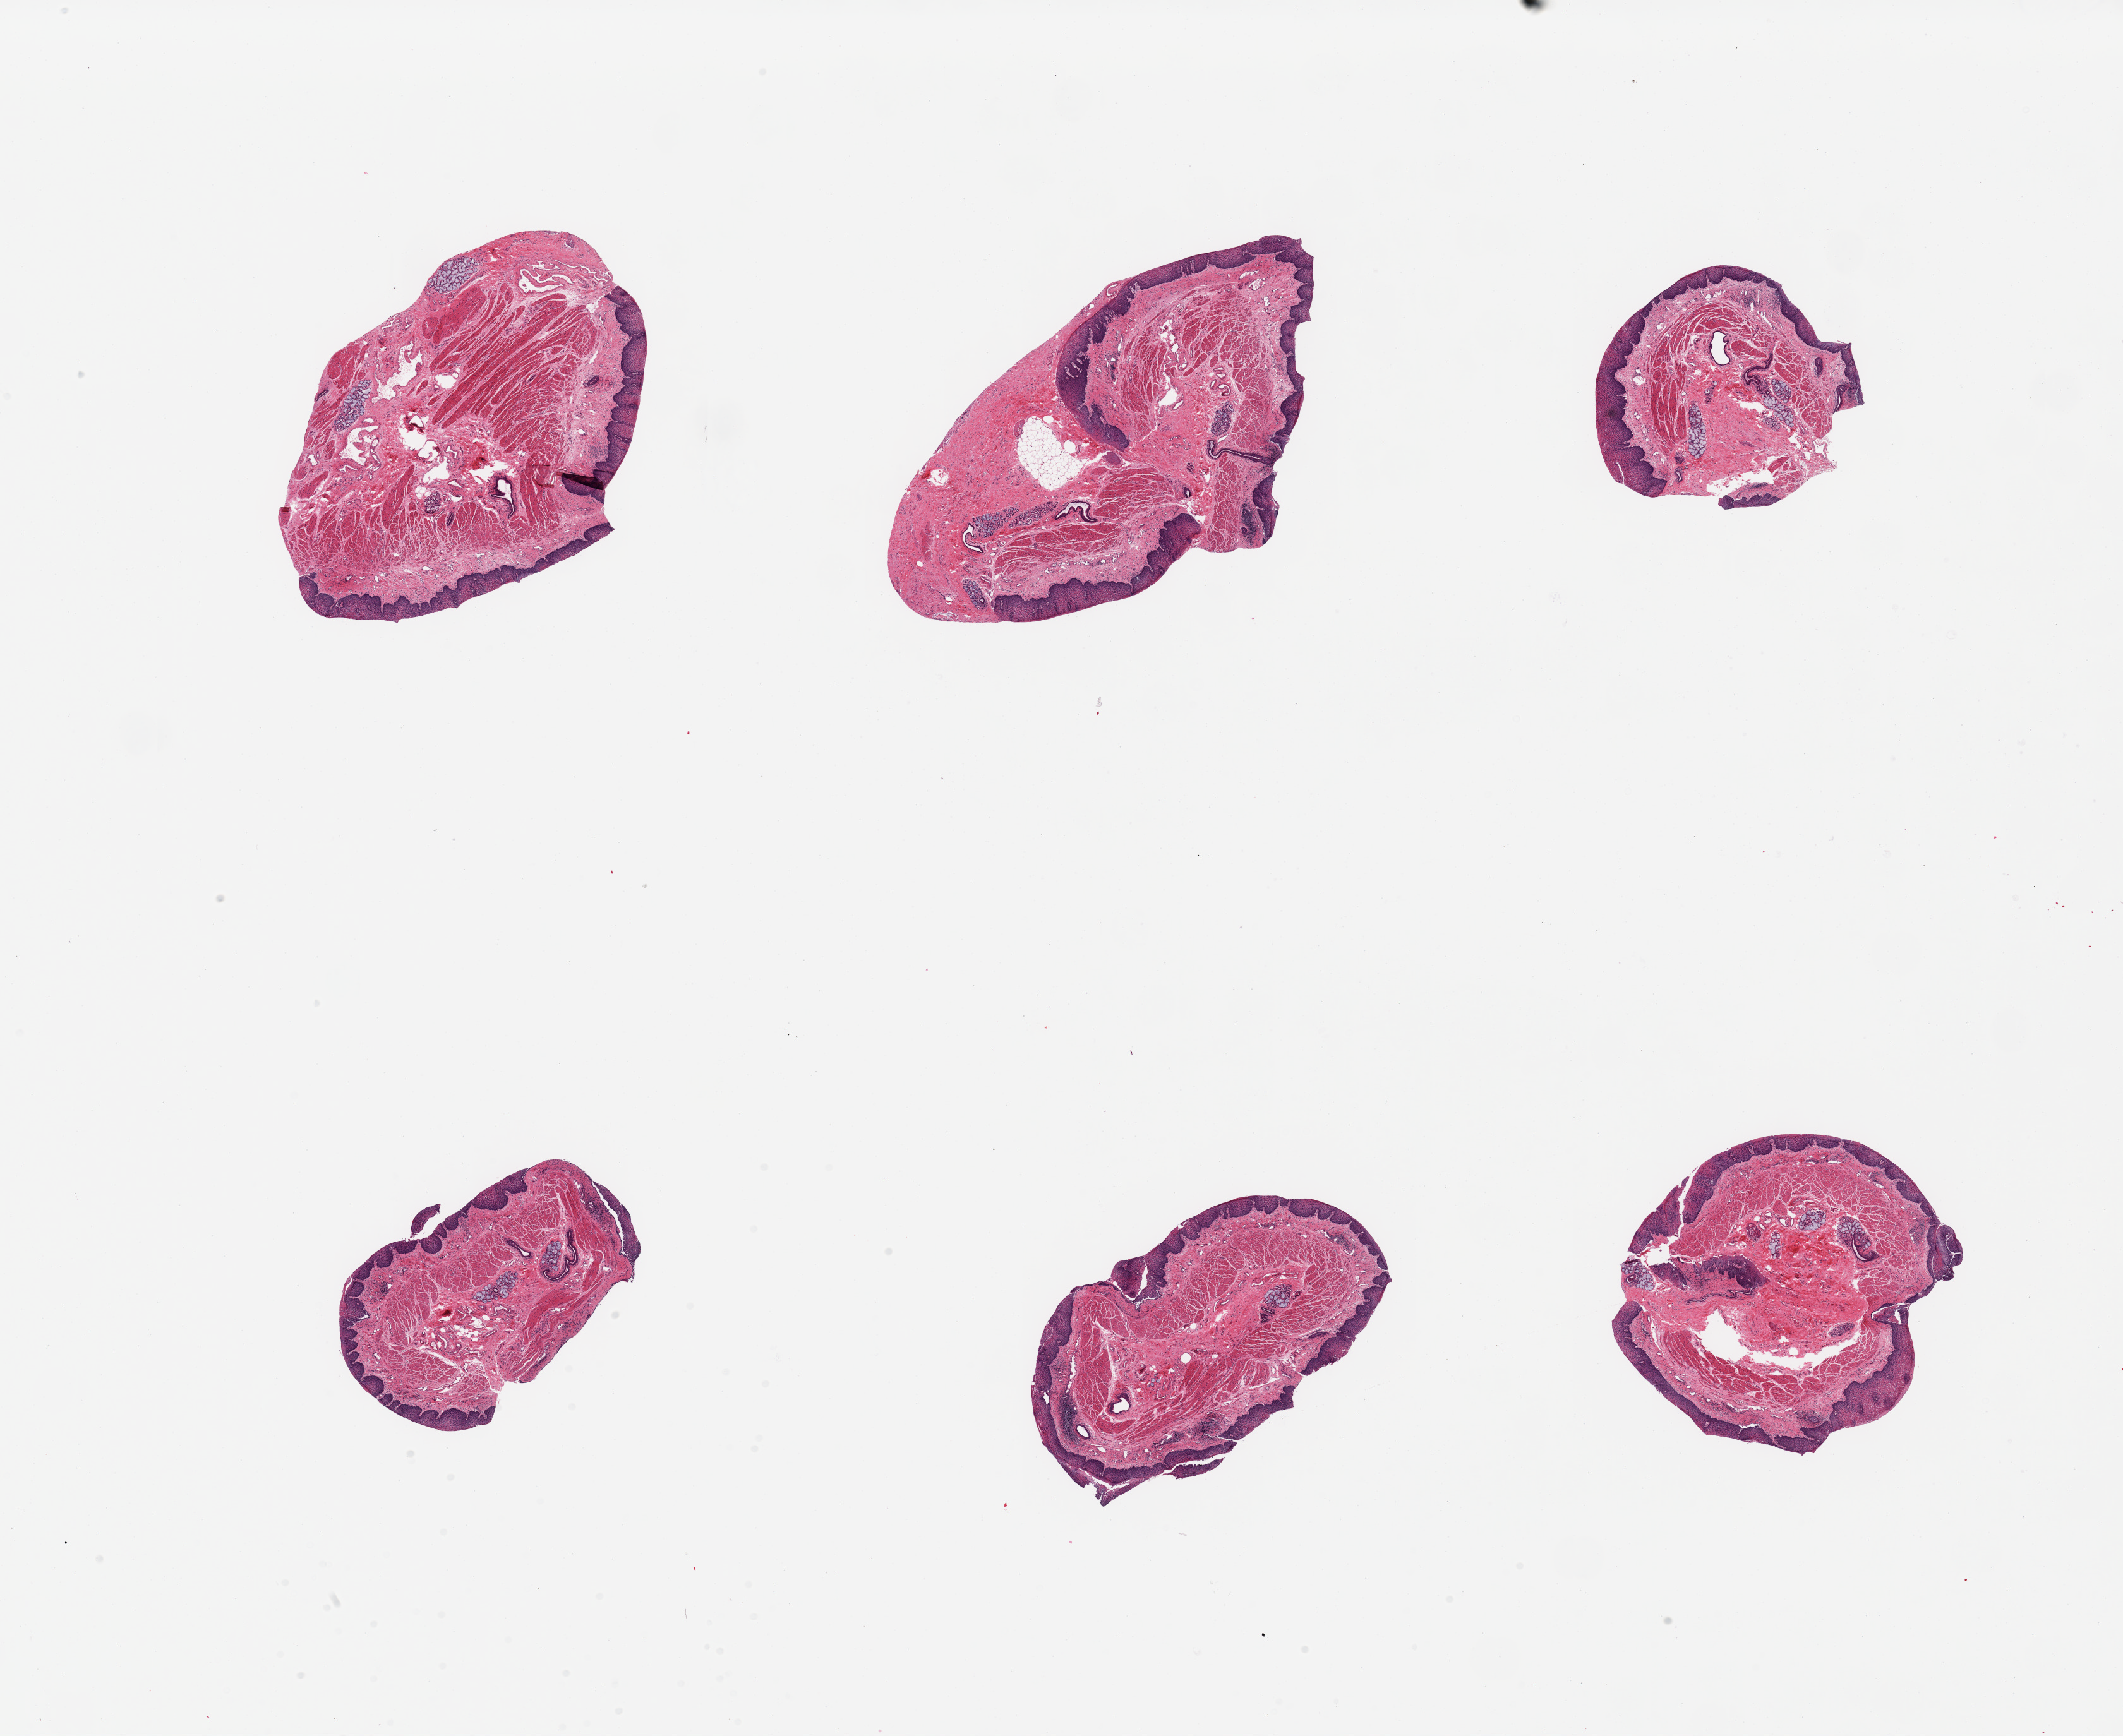
Hematoxylin and eosin (H&E) whole-slide image, brightfield, a low-resolution overview of the entire scanned area, about 26.6 x 21.7 mm (slide scanned at 20x); PAXgene-fixed, paraffin-embedded tissue; target tissue: esophageal mucous membrane; donor tissue sample. Male donor.
Reviewer comment on this tissue sample: 6 pieces, squamous mucosa is 0.2-0.4mm, ~20-25% thickness; submucosal mucus glands.